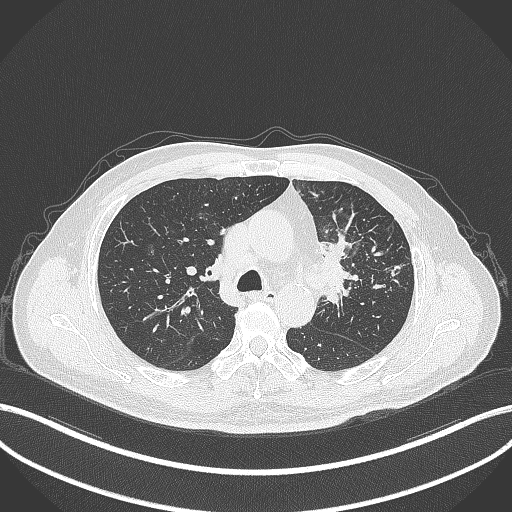
Chest CT, one axial slice. Position 234 of 386 along the scan axis. Reconstruction kernel B70f. 120 kVp. Lung window (W 1500 / L -600 HU). 1 mm slice thickness. 512 × 512 image matrix, field of view 400 × 400 mm. Patient: male, 69 years. From the clinical record (not read from this slice): clinical TNM (as recorded): T2a N2 M0.
Outlined on this slice (bounding box drawn by a radiologist):
- lung tumour (recorded histology: adenocarcinoma): box from (x=313, y=232) to (x=366, y=311) px